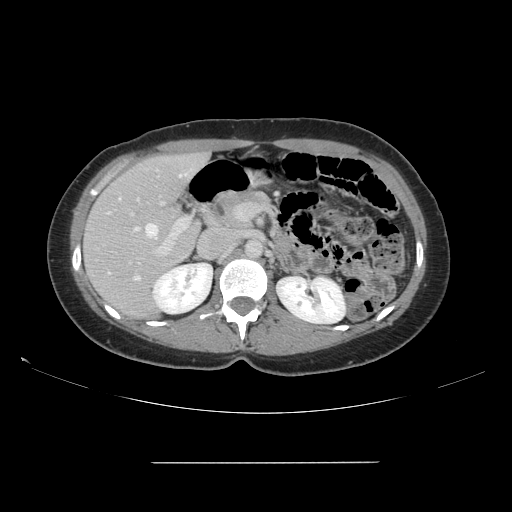
Contrast-enhanced abdominal CT, one axial slice; slice 87 of 151 in the series (ordered by position); 120 kVp; intravenous contrast given; soft-tissue window (W 400 / L 40 HU); 2.5 mm slice thickness; 512 × 512 image matrix. Female patient, age 46 years. Case-level facts recorded for this patient, not image findings: diagnosis: colorectal cancer liver metastases, imaged before liver resection; multiple liver metastases: yes; largest metastasis: 3 cm; chemotherapy before resection: no.
Annotated regions visible in this slice (outlined manually by an expert reader):
- hepatic veins: bounding box <107,173,187,279> (left, top, right, bottom; pixels)
- liver: <84,154,208,320>
- planned liver remnant (the part of the liver to remain after resection): <93,154,201,304>
- portal vein (with intrahepatic branches): <130,196,245,257>